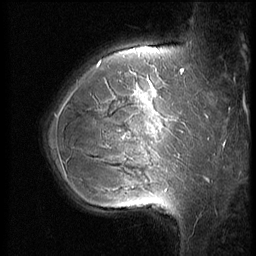
Breast MRI (dynamic contrast-enhanced), one sagittal slice. Position 45 of 56 along the scan axis. 3 images stored at this slice position (order not interpretable as contrast timing). 1.5 T. TE 4.2 ms, TR 9 ms. 256 × 256 image matrix. Patient: female, 35 years. From the clinical record (not read from this slice): setting: breast cancer imaged before/during neoadjuvant chemotherapy; receptor status: HR-positive, HER2-negative.
Annotated regions visible in this slice (semi-automatic segmentation, software-assisted and operator-edited):
- analysis volume of interest (the breast-tissue region the enhancement analysis was run in; not a lesion): bounding box <63,60,190,218> (left, top, right, bottom; pixels)
- tumour enhancement mask (voxels above the 140 % enhancement threshold inside the analysis volume of interest): <98,66,173,139>